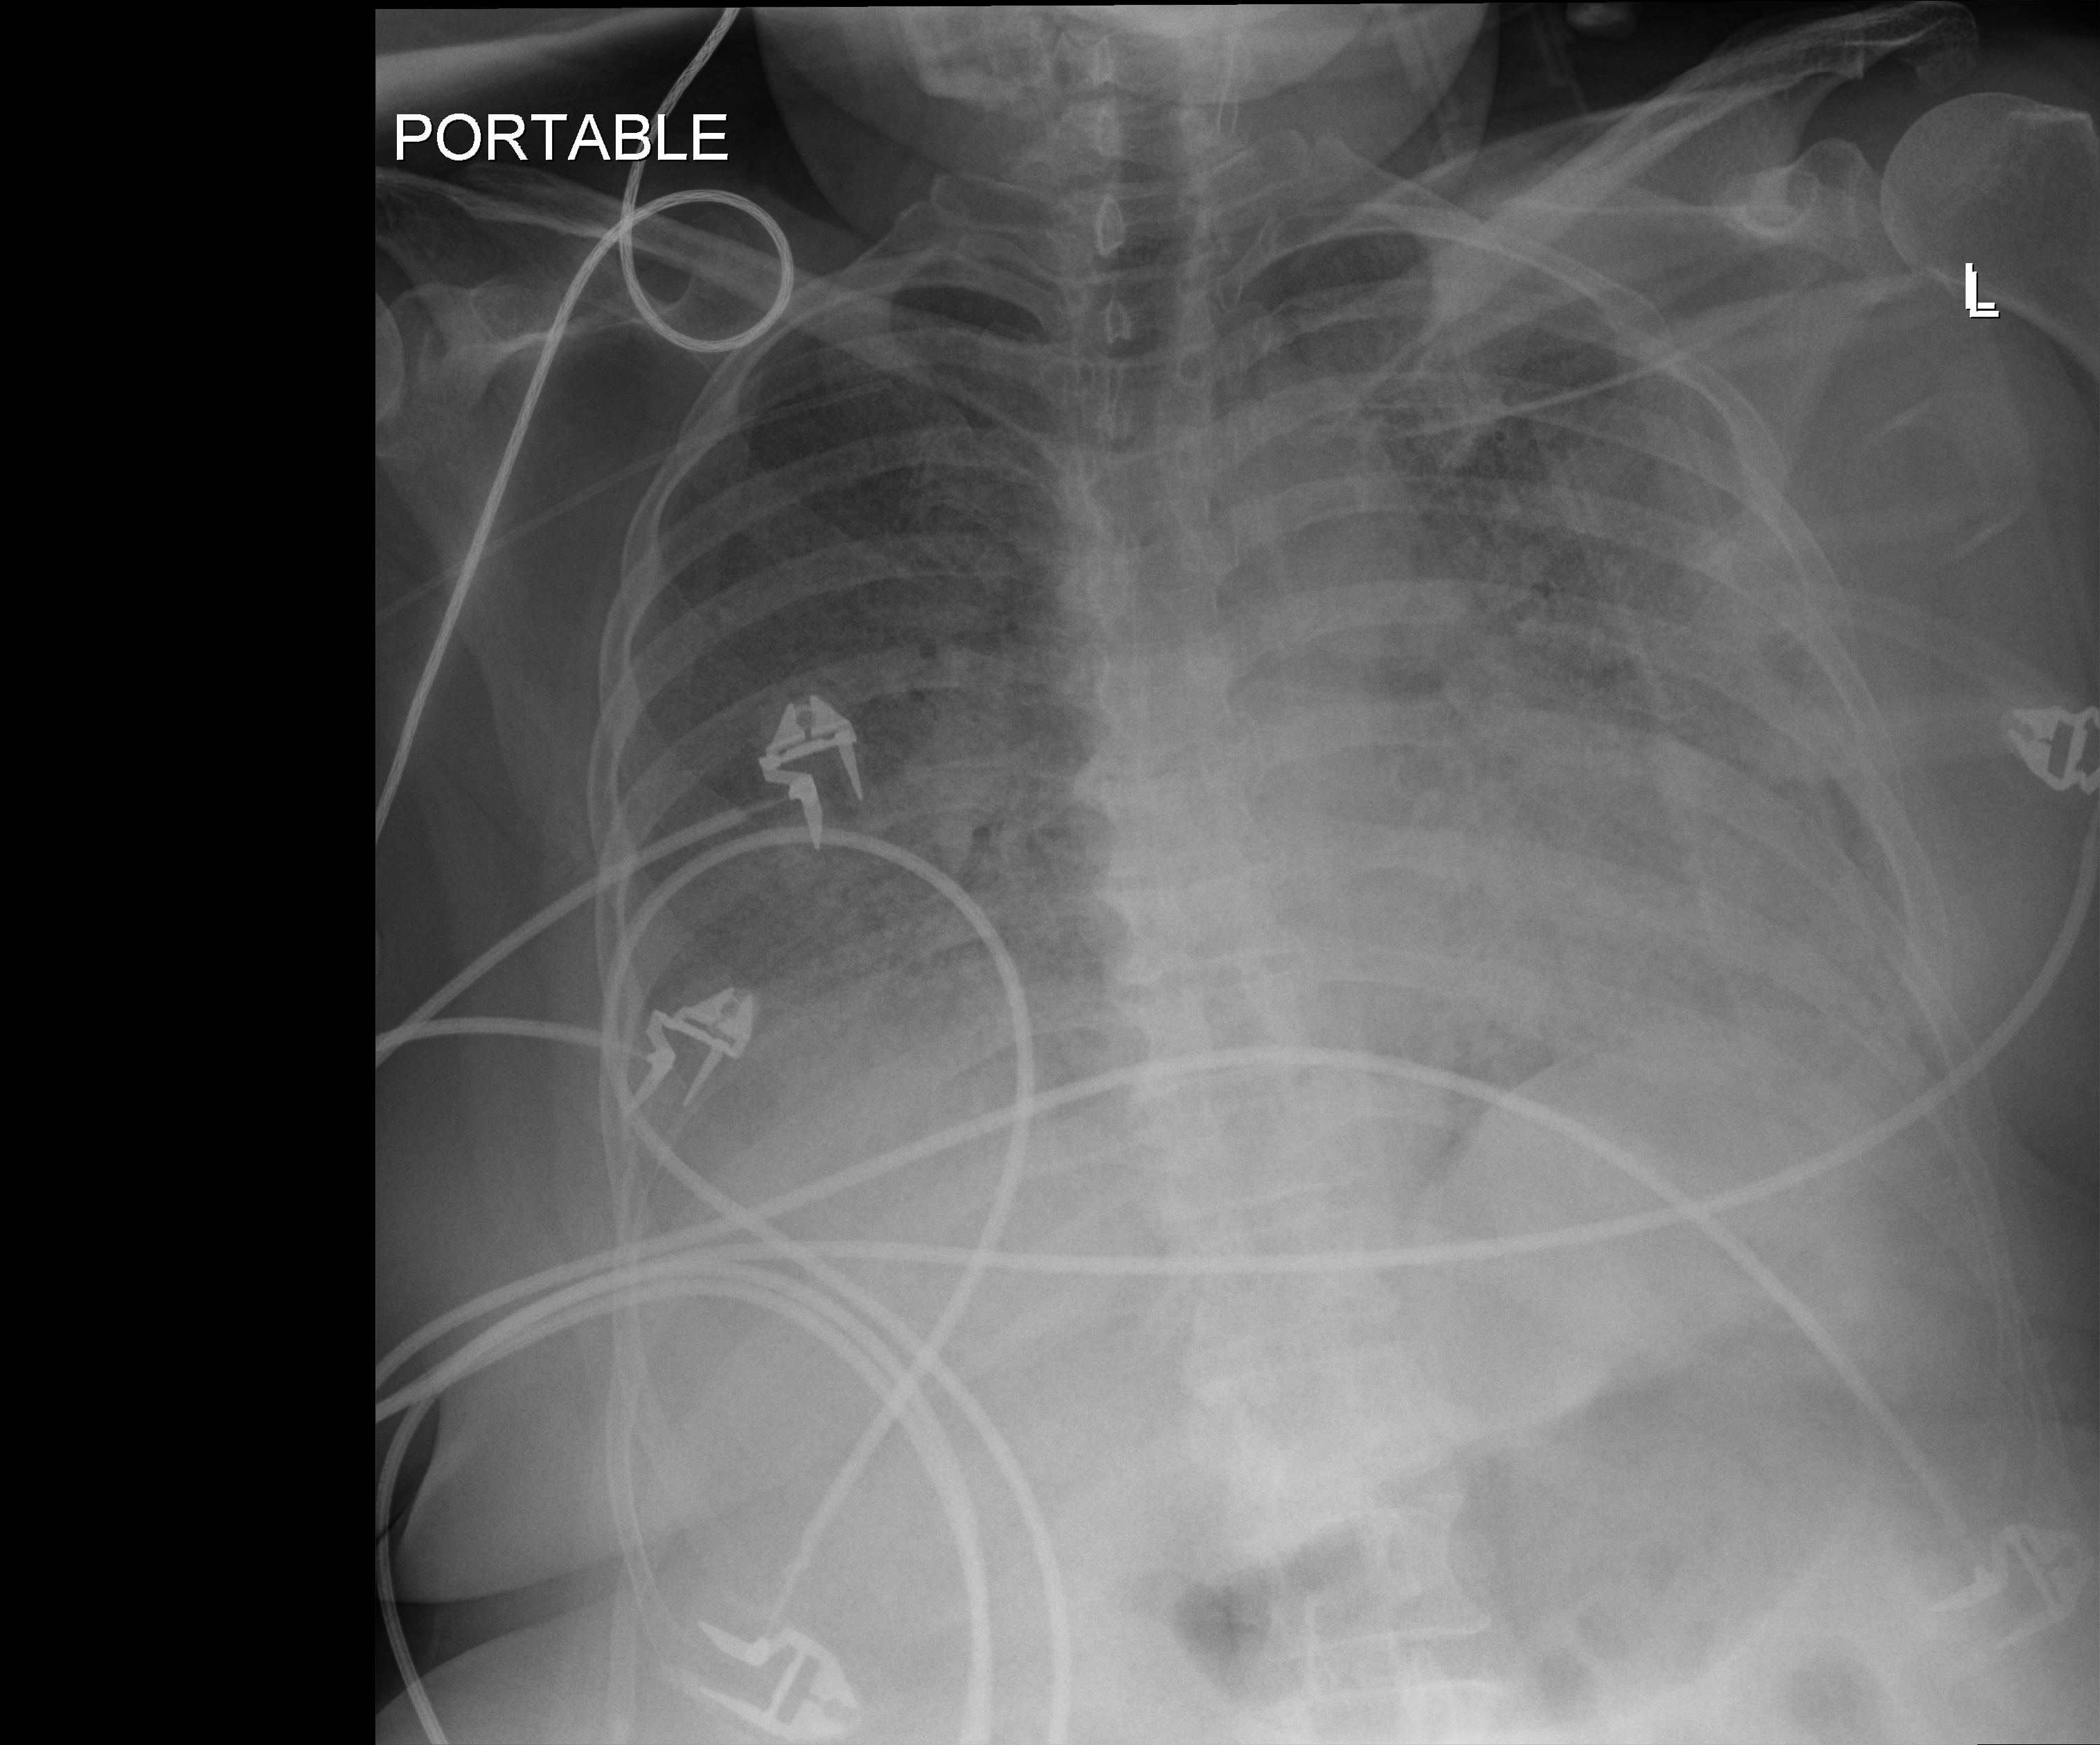
Chest radiograph (digital radiography), anteroposterior (AP) projection. Patient hospitalised with COVID-19; female, aged 60–74 years.
Admission-level facts for this patient (not findings on this image; timing relative to this image not recorded):
- mechanically ventilated during this hospital stay: yes
- smoking status (admission record): former
- COPD (admission record): no